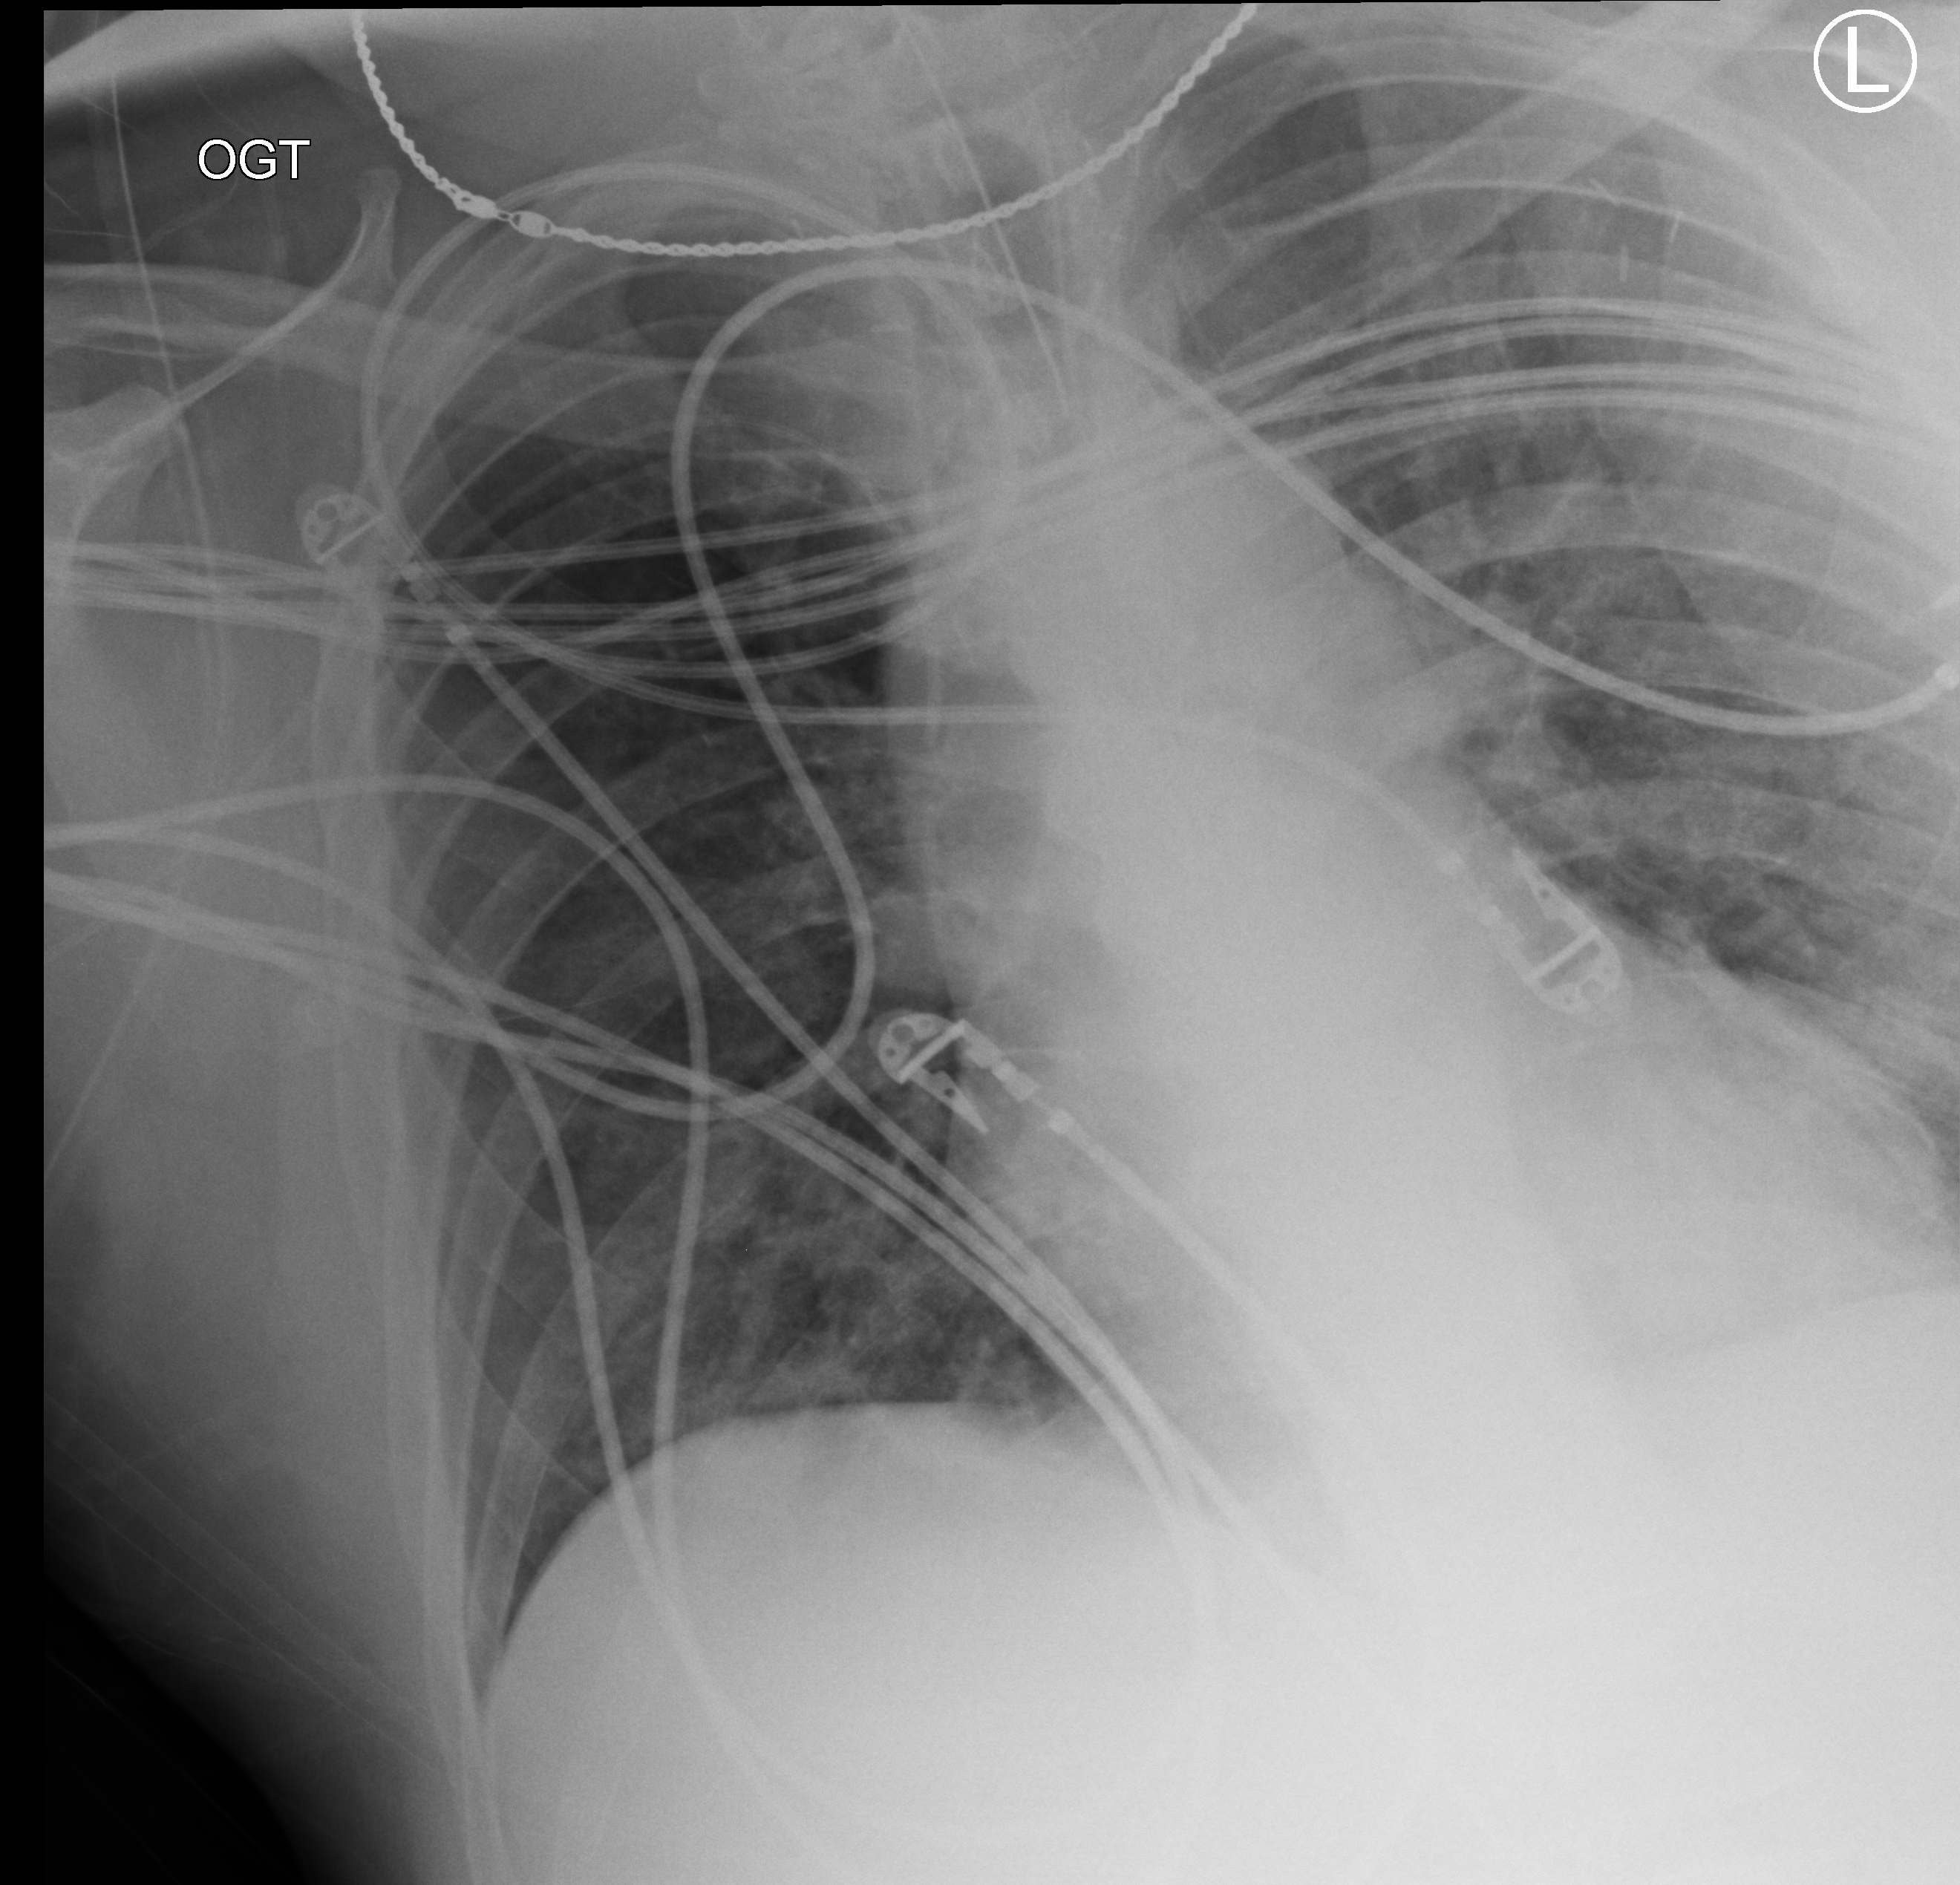
Chest X-ray (portable); anteroposterior (AP) projection. Patient hospitalised with COVID-19, aged 18–59 years.
From the hospital-stay record, not from the radiograph (when in the stay this image was taken is not recorded):
- admitted to intensive care during this hospital stay: yes
- mechanically ventilated during this hospital stay: yes